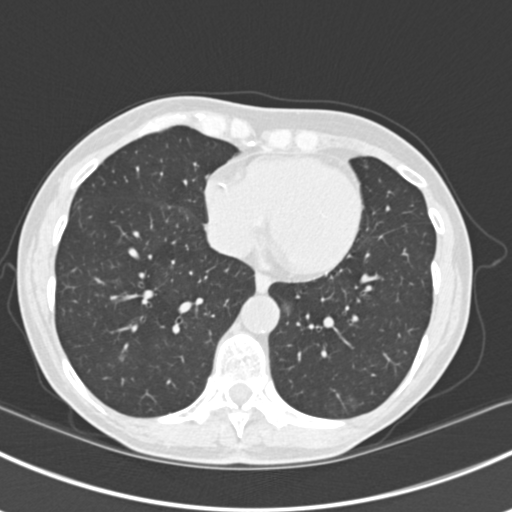
Axial slice from a low-dose chest CT screening exam; baseline annual screen; lung window (W 1500 / L -600 HU); slice 130 of 224 in the series. Female participant, aged 63 years at enrolment. Current smoker at enrolment.
Expert-annotated lung lesion, bounding box (x1, y1, x2, y2) in pixels: (96, 312, 149, 366). The screening reader recorded 10 non-calcified nodules or masses ≥4 mm on this exam; which of them this box marks is not recorded. Later outcome: lung cancer diagnosed 751 days after this screen (after the third annual screen) — bronchiolo-alveolar adenocarcinoma, NOS, right upper lobe, right middle lobe, right lower lobe, left upper lobe, left lower lobe, moderately differentiated (G2), stage IV (AJCC 6th edition).